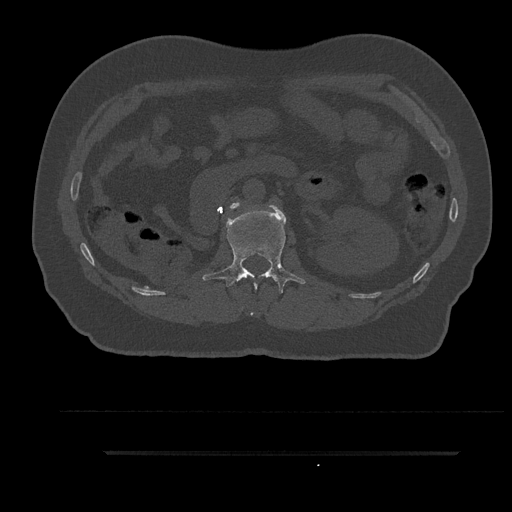
CT including the spine, one axial slice. Reconstruction kernel Br40s/3. 120 kVp. Bone window (W 1800 / L 400 HU). 0.5 mm slice thickness. 512 × 512 image matrix, field of view 432 × 432 mm. Male patient, age 63 years. From the clinical record (not read from this slice): primary cancer: renal; vertebrae with lytic lesions (as recorded): T8.
Outlined on this slice (semi-automatically segmented with operator editing):
- L1 vertebra: box from (x=203, y=205) to (x=305, y=315) px
- L2 vertebra: (x=230, y=202)–(x=239, y=209)